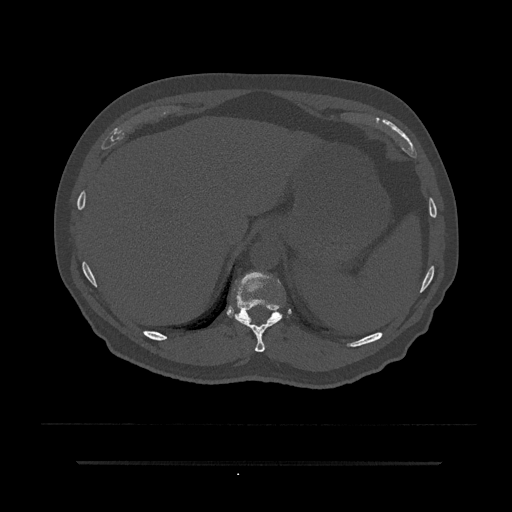
CT including the spine, one axial slice. Position 299 of 797 along the scan axis. 120 kVp. Bone window (W 1800 / L 400 HU). 0.5 mm slice thickness. 512 × 512 image matrix, field of view 464 × 464 mm. Male patient, age 59 years. From the clinical record (not read from this slice): primary cancer: bile ducts; vertebrae with lytic lesions (as recorded): T10.
Structures marked on this image (semi-automatically segmented with operator editing):
- T10 vertebra: bounding box (x1, y1, x2, y2) in pixels: (235, 316, 282, 352)
- T11 vertebra: (229, 272, 290, 323)